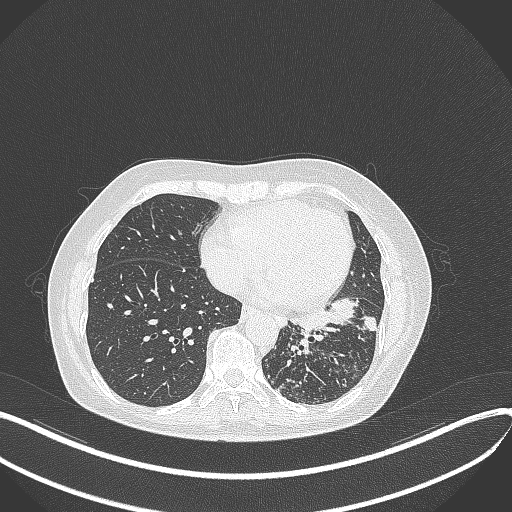
Chest CT, one axial slice; position 143 of 429 along the scan axis; reconstruction kernel B70f; lung window (W 1500 / L -600 HU); 1 mm slice thickness; 512 × 512 image matrix, field of view 400 × 400 mm. Female patient, age 63 years. From the clinical record (not read from this slice): clinical TNM (as recorded): T1b N0 M0; histopathological grade: G2-3.
Structures marked on this image (rectangle marked by the reading radiologist):
- lung tumour (recorded histology: adenocarcinoma): bounding box [x1, y1, x2, y2] px = [288, 292, 377, 336]